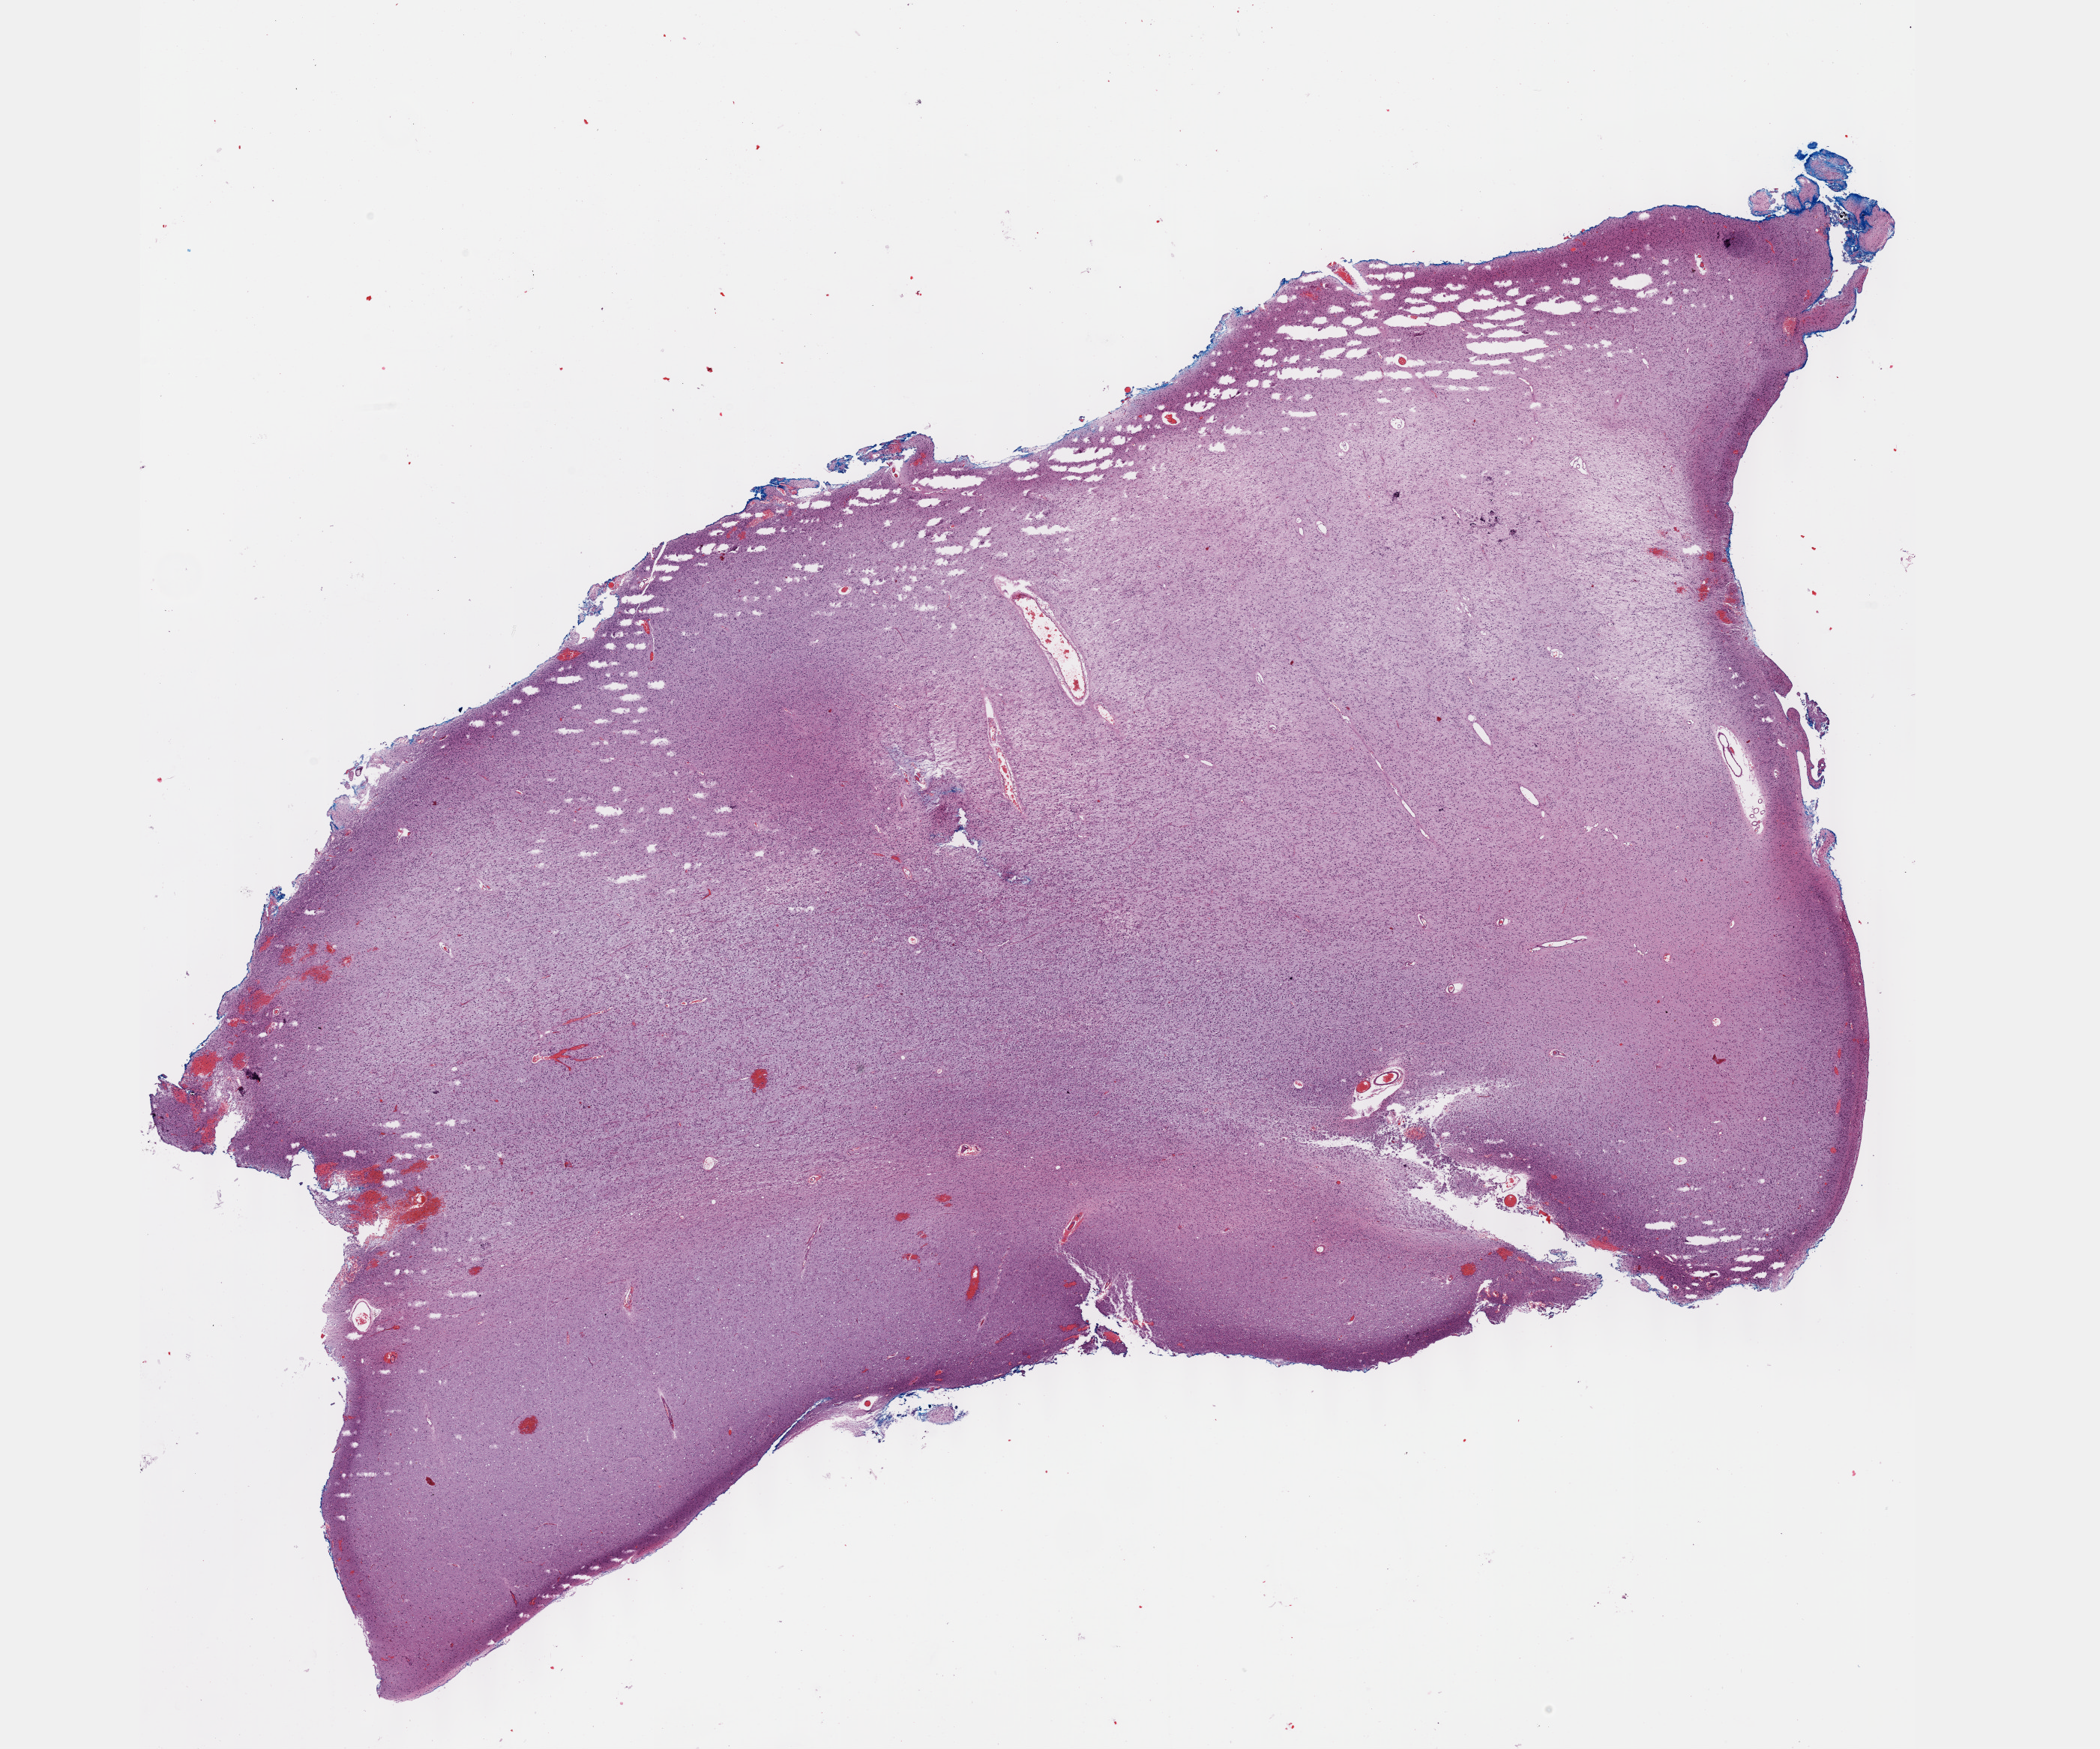
Hematoxylin and eosin (H&E) stained whole-slide image — shown as a low-resolution overview of the whole scanned area (about 22.6 x 18.9 mm), formalin-fixed paraffin-embedded (FFPE) diagnostic section, sample: primary tumour, brain. Patient: female, age at initial diagnosis 39 years.
Diagnosis: Astrocytoma, NOS (cerebrum).